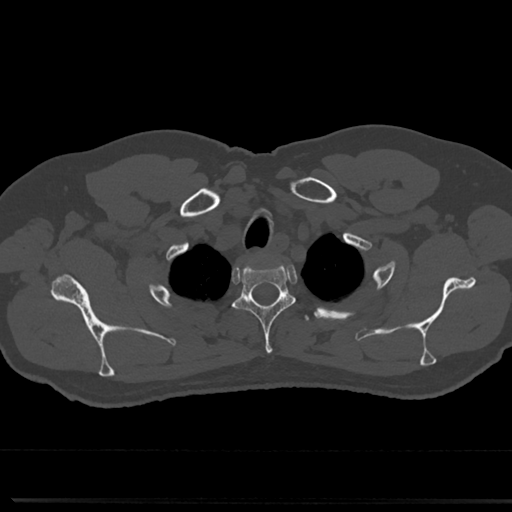
CT including the spine, one axial slice. Slice 633 of 817 in the series (ordered by position). Reconstruction kernel Br40s/3. 120 kVp. Bone window (W 1800 / L 400 HU). 0.5 mm slice thickness. 512 × 512 image matrix. Patient: male, 61 years. Case-level facts recorded for this patient, not image findings: primary cancer: prostate.
Annotated regions visible in this slice (semi-automatic segmentation, software-assisted and operator-edited):
- T2 vertebra: bounding box [x1, y1, x2, y2] px = [234, 257, 294, 356]
- T3 vertebra: [297, 312, 311, 325]